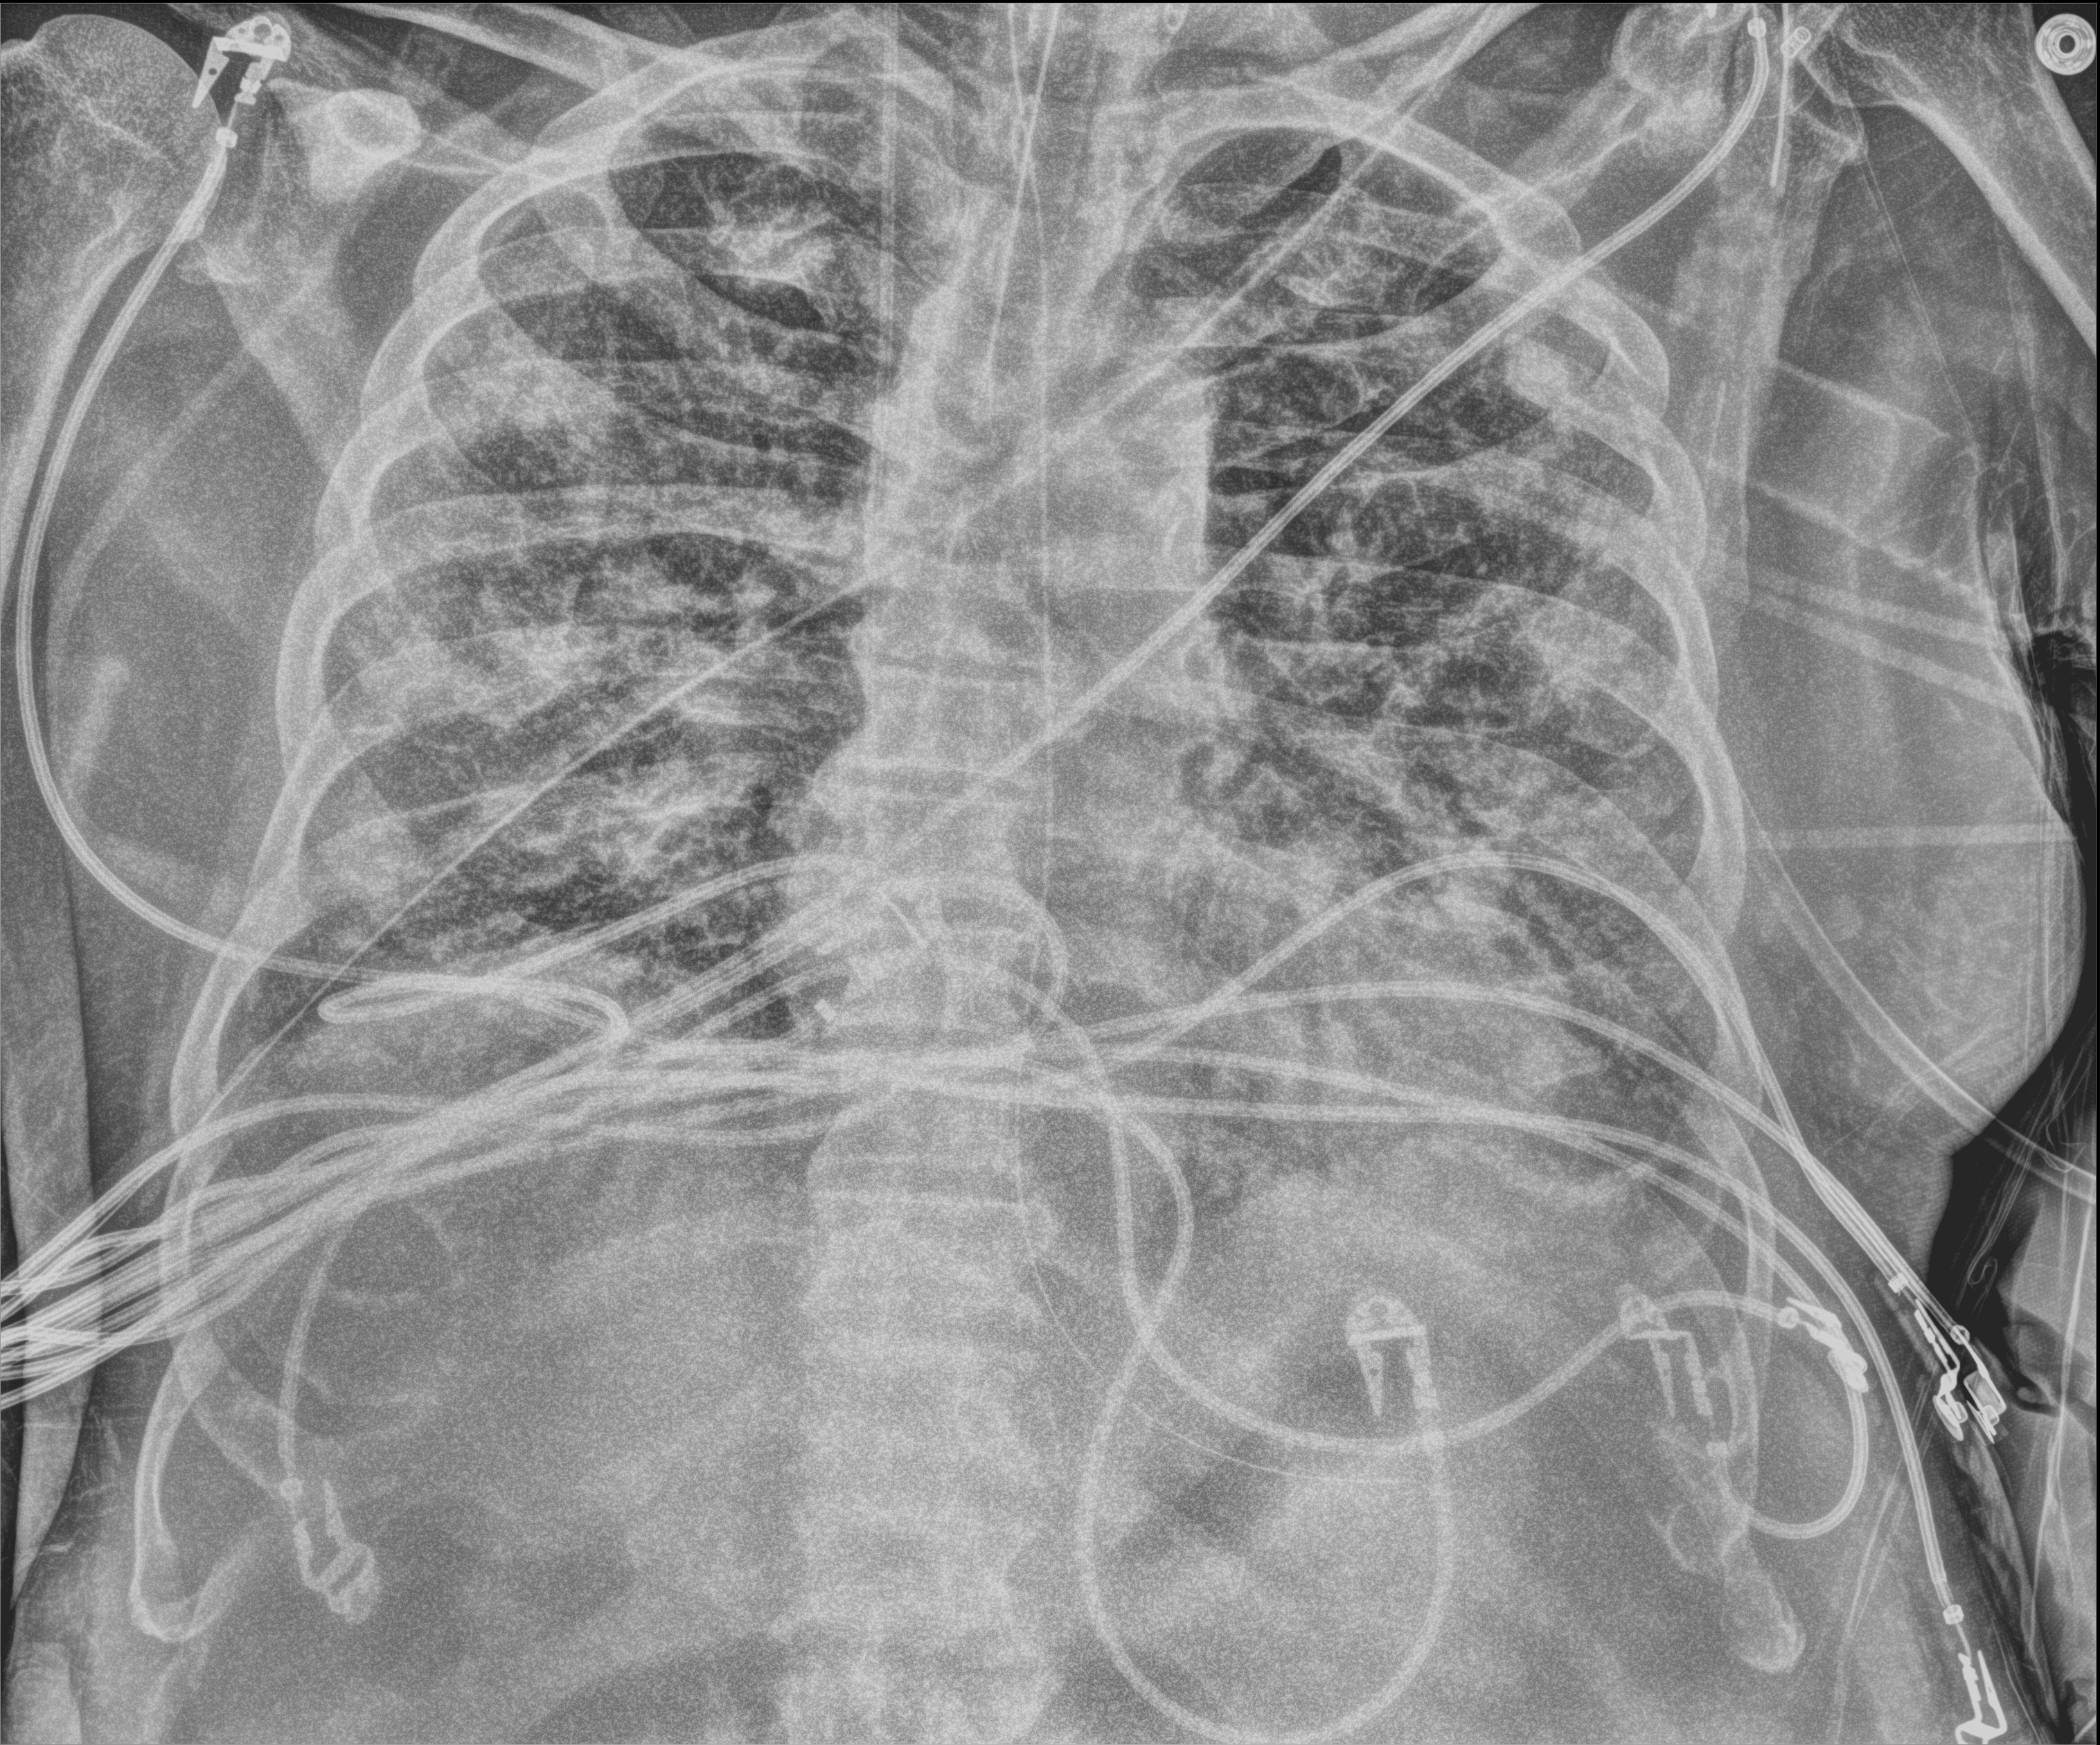
Chest radiograph (digital radiography). Patient hospitalised with COVID-19; male, aged 75–90 years.
Hospital-stay facts (about this admission, not read from this image; timing relative to this image not recorded): admitted to intensive care during this hospital stay: yes; length of hospital stay: 33 days; mechanically ventilated during this hospital stay: yes.